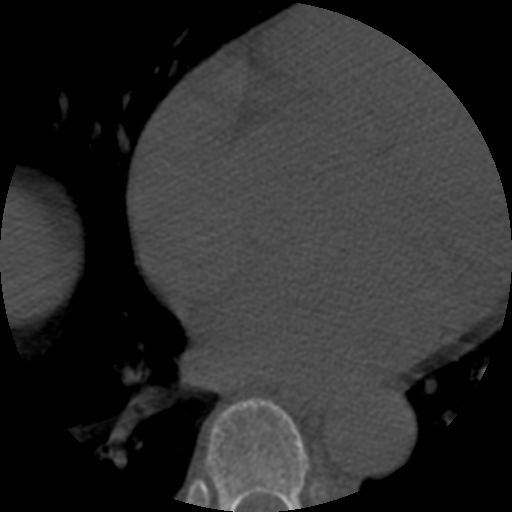
CT including the spine, one axial slice. Position 336 of 508 along the scan axis. Reconstruction kernel STANDARD. Bone window (W 1800 / L 400 HU). 512 × 512 image matrix. Patient age 57 years. Case-level facts recorded for this patient, not image findings: primary cancer: prostate.
Annotated regions visible in this slice (semi-automatically segmented with operator editing):
- T7 vertebra: box from (x=207, y=398) to (x=309, y=512) px